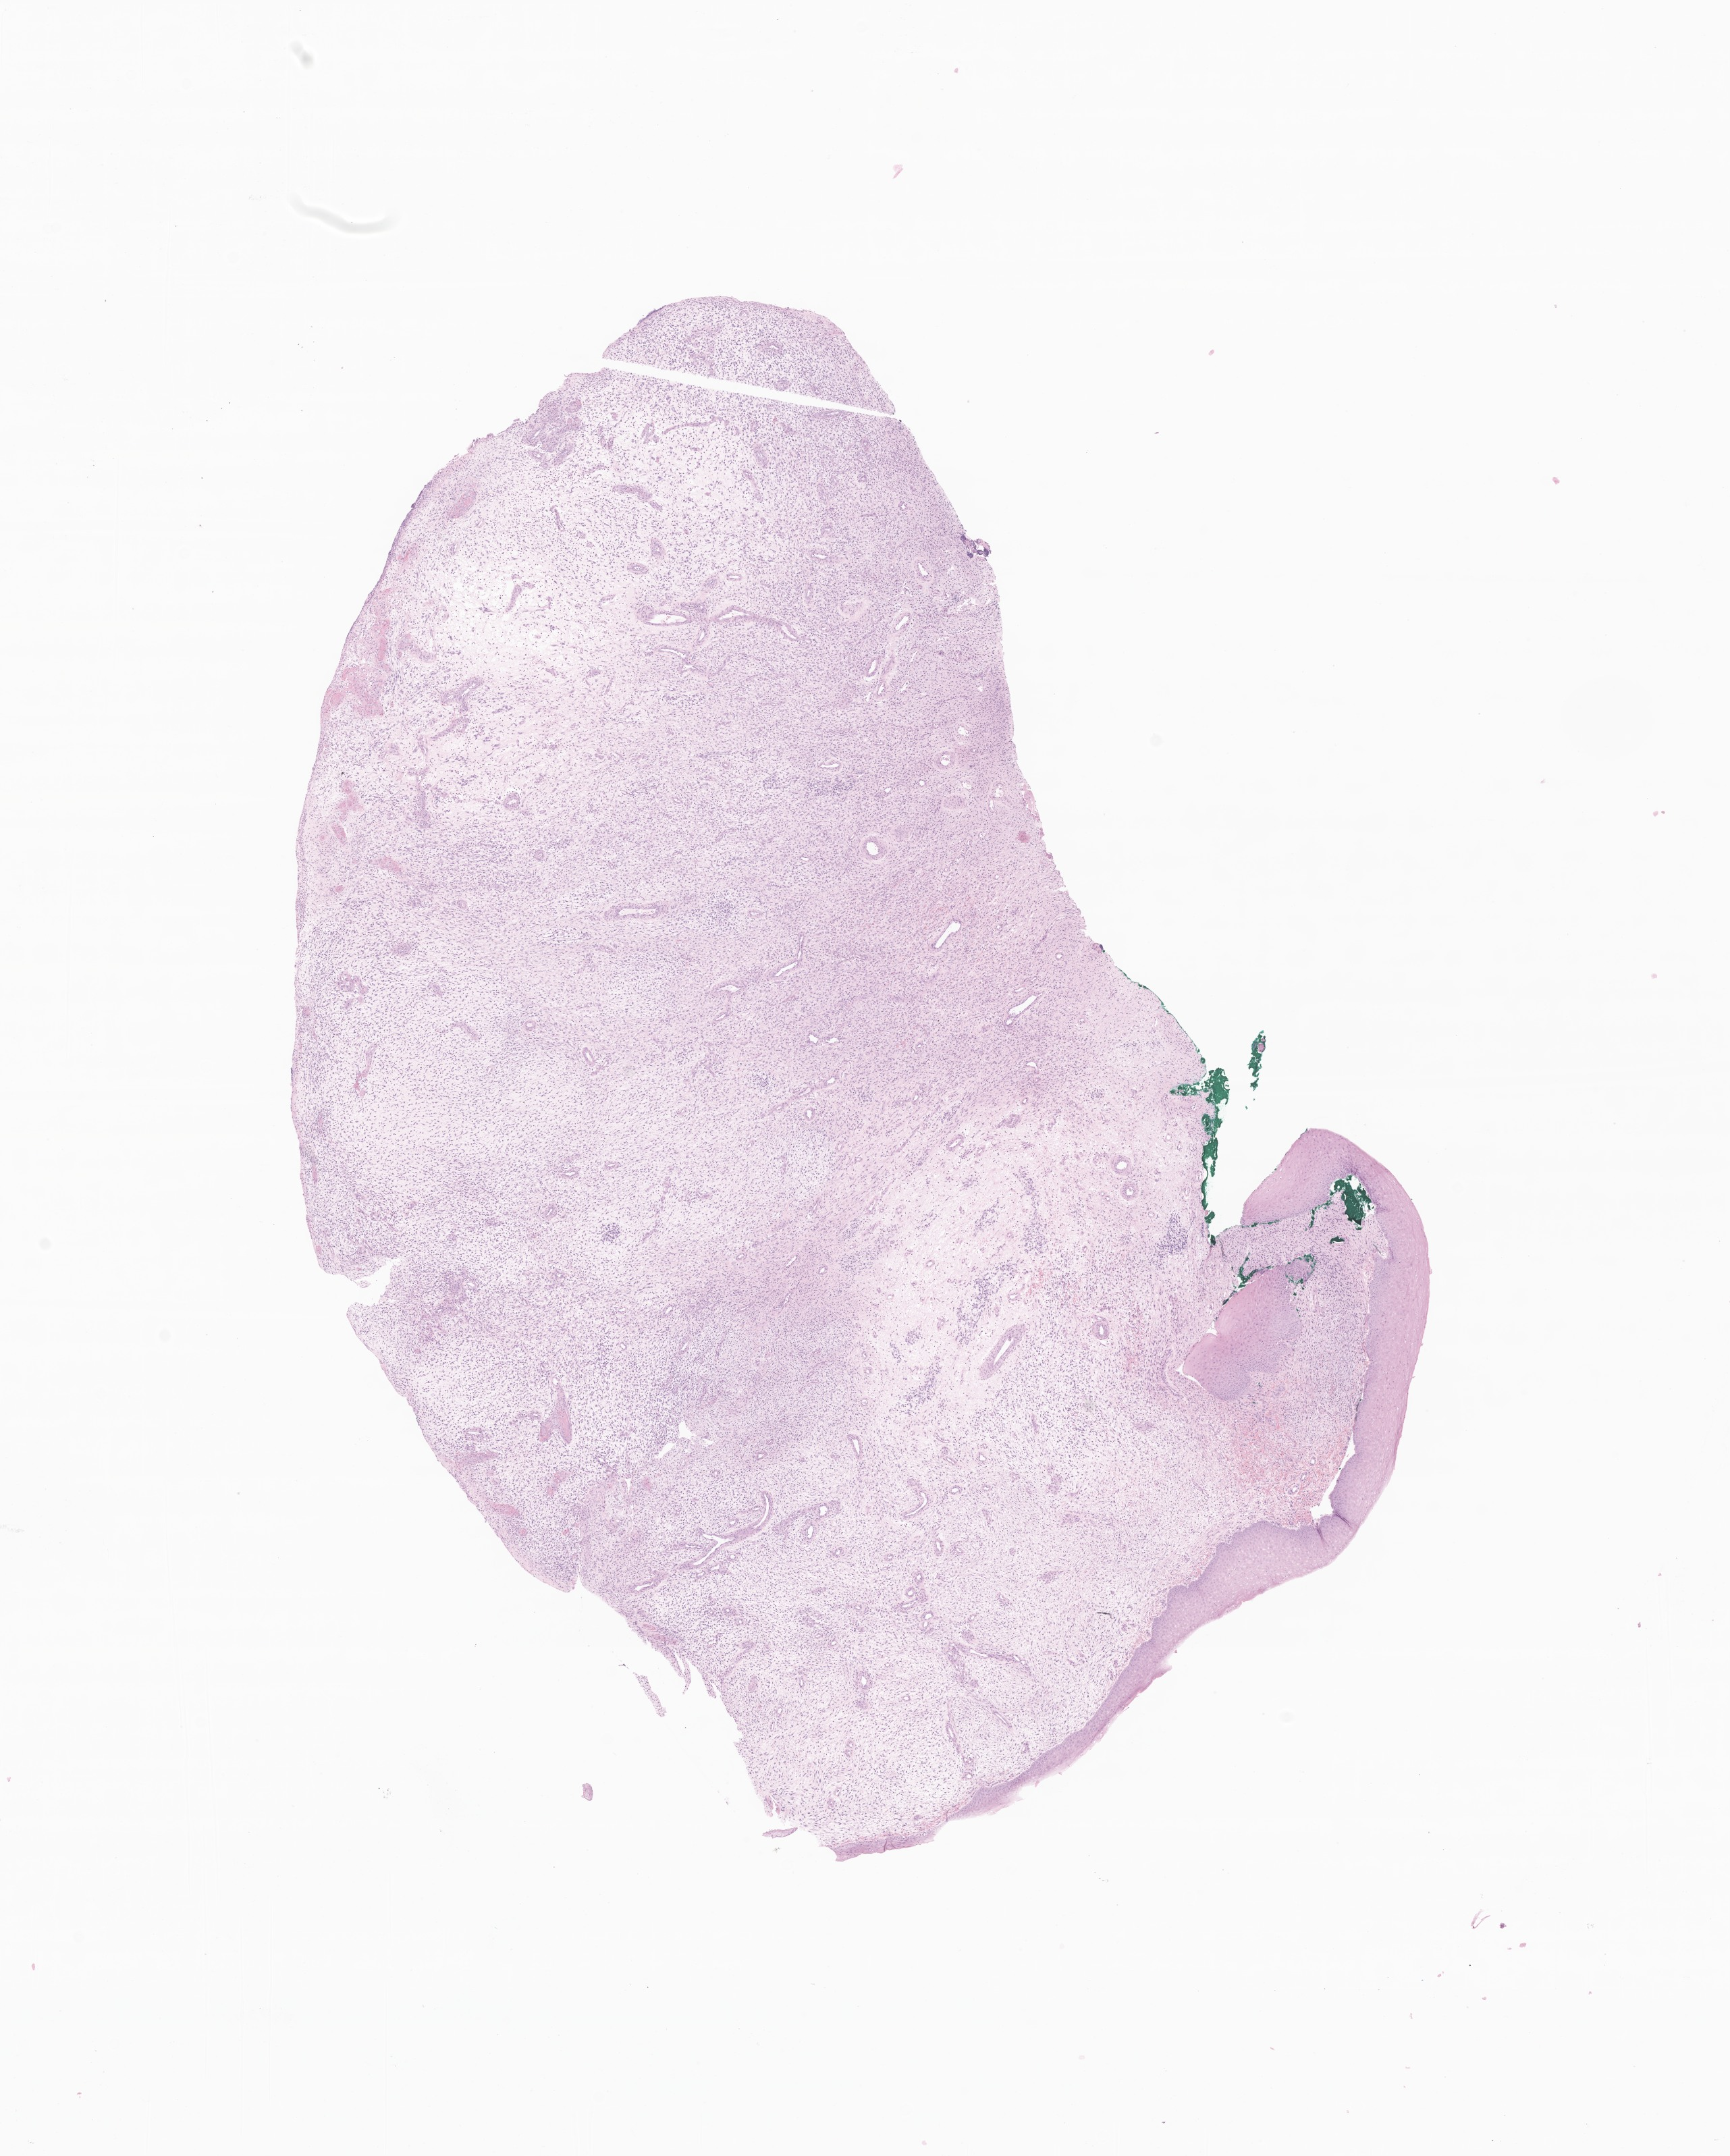
Whole-slide image, H&E stain of tumor tissue from the vagina, whole scanned area (about 10.8 x 13.5 mm) shown as a low-resolution overview; formalin-fixed, paraffin-embedded (FFPE) tissue. Patient: female, age 620 days (about 1.7 years).
Diagnosis (ICD-O-3 morphology term): Embryonal rhabdomyosarcoma, NOS.